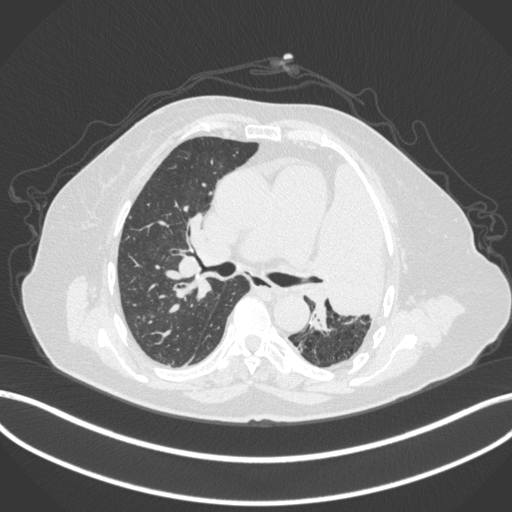
Chest CT, one axial slice; slice 235 of 399 in the series (ordered by position); lung window (W 1500 / L -600 HU); 1 mm slice thickness; 512 × 512 image matrix, field of view 400 × 400 mm. Patient: female, 75 years. Case-level facts recorded for this patient, not image findings: clinical TNM (as recorded): T3 N3 M1.
Outlined on this slice (bounding box drawn by a radiologist):
- lung tumour (recorded histology: adenocarcinoma): bounding box (x1, y1, x2, y2) in pixels: (312, 153, 396, 324)